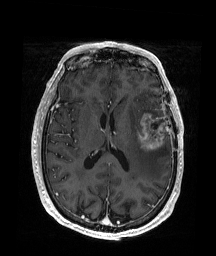
Brain MRI from a brain-tumour surgery series, one axial slice; slice 85 of 176 in the series (ordered by position); T1-weighted post-contrast; 1 mm slice thickness; 216 × 256 image matrix. Case-level facts recorded for this patient, not image findings: histopathology: Glioblastoma; WHO grade: 4; IDH mutation: no; tumour location: Left Frontal.
Annotated regions visible in this slice (expert manual segmentation):
- tumour: bounding box (x1, y1, x2, y2) in pixels: (136, 113, 168, 151)